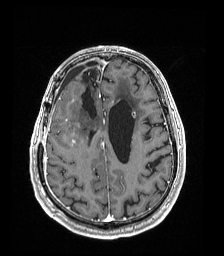
Brain MRI from a brain-tumour surgery series, one axial slice; T1-weighted post-contrast; 1 mm slice thickness; 224 × 256 image matrix, field of view 224 × 256 mm. From the clinical record (not read from this slice): histopathology: Astrocytoma; WHO grade: 4; IDH mutation: yes; tumour location: Right Frontal.
Annotated regions visible in this slice (expert manual segmentation):
- previous resection cavity: bounding box [x1, y1, x2, y2] px = [81, 68, 98, 119]
- tumour: [72, 139, 76, 145]